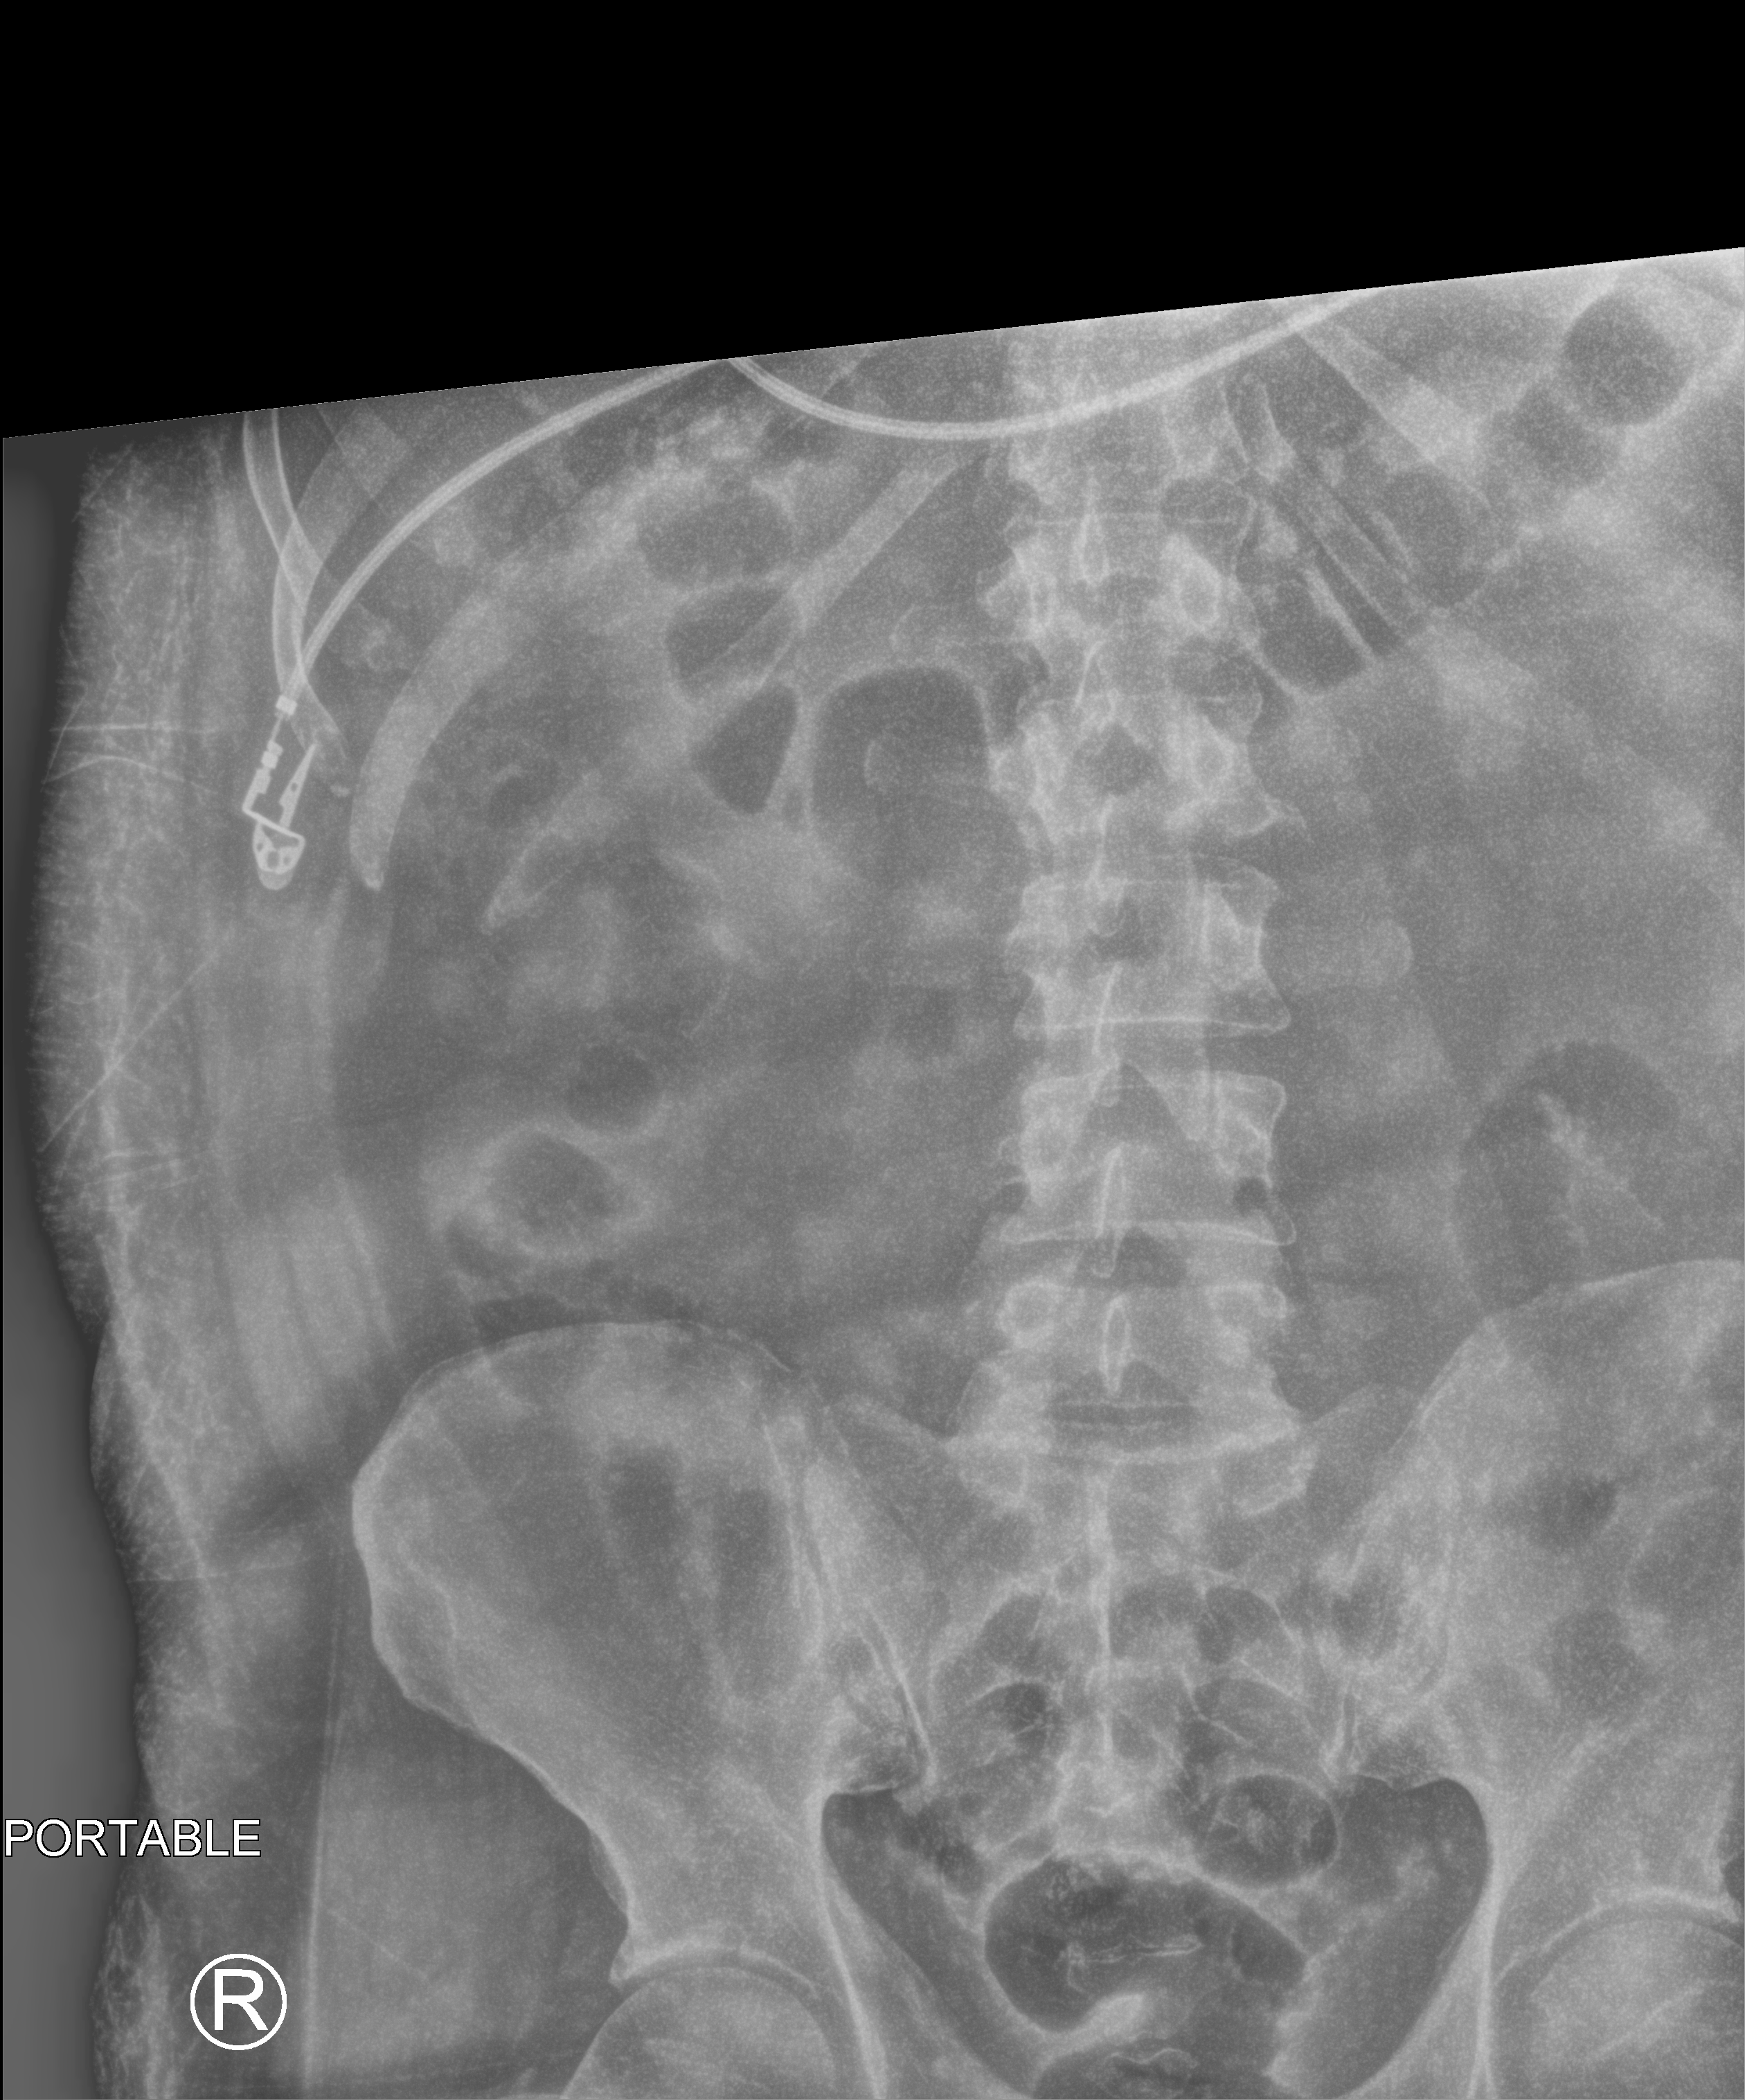
Portable abdomen radiograph; anteroposterior (AP) projection. Patient hospitalised with COVID-19; male, aged 18–59 years.
Admission-level facts for this patient (not findings on this image; timing relative to this image not recorded):
- length of hospital stay: 39 days